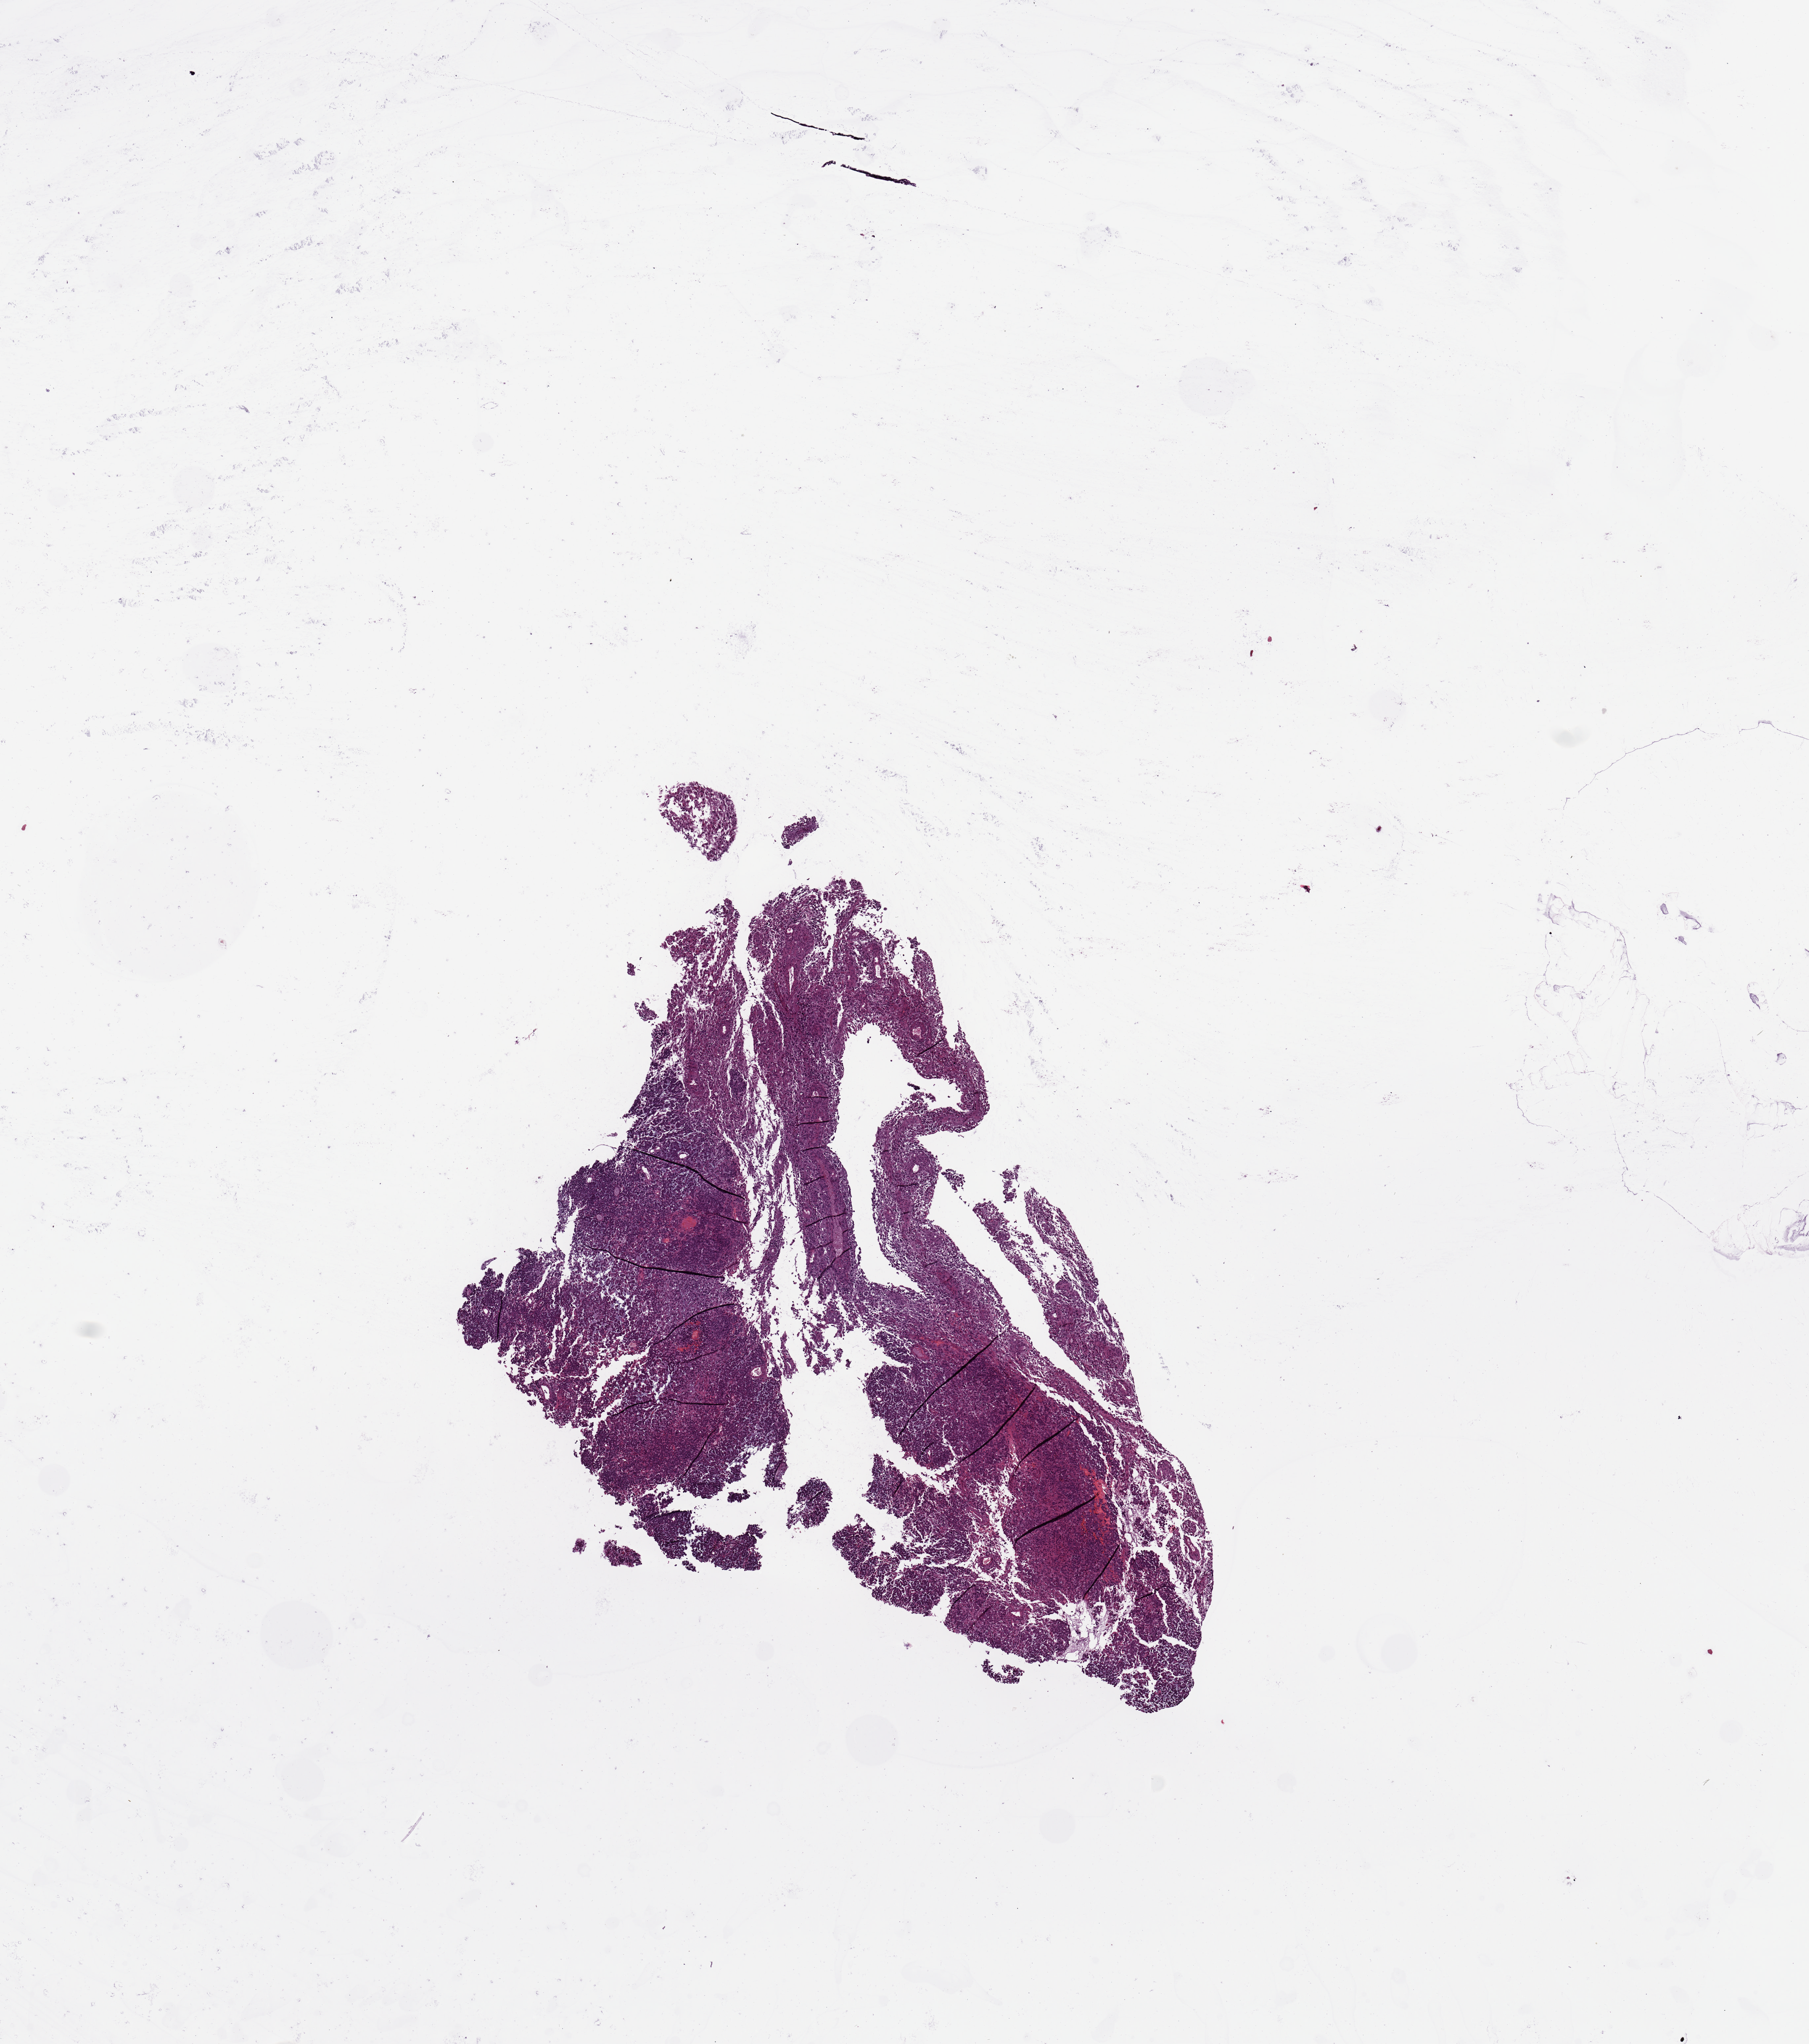
Whole-slide histology image, H&E — low-resolution overview of the scanned area, about 10.8 x 12.2 mm (acquisition: 20x scan); tumour tissue sample, sampled site: brain. Male, 53 y/o. Slide review estimates, as recorded: tumour nuclei 85%, necrosis 3%.
* histologic diagnosis: Glioblastoma